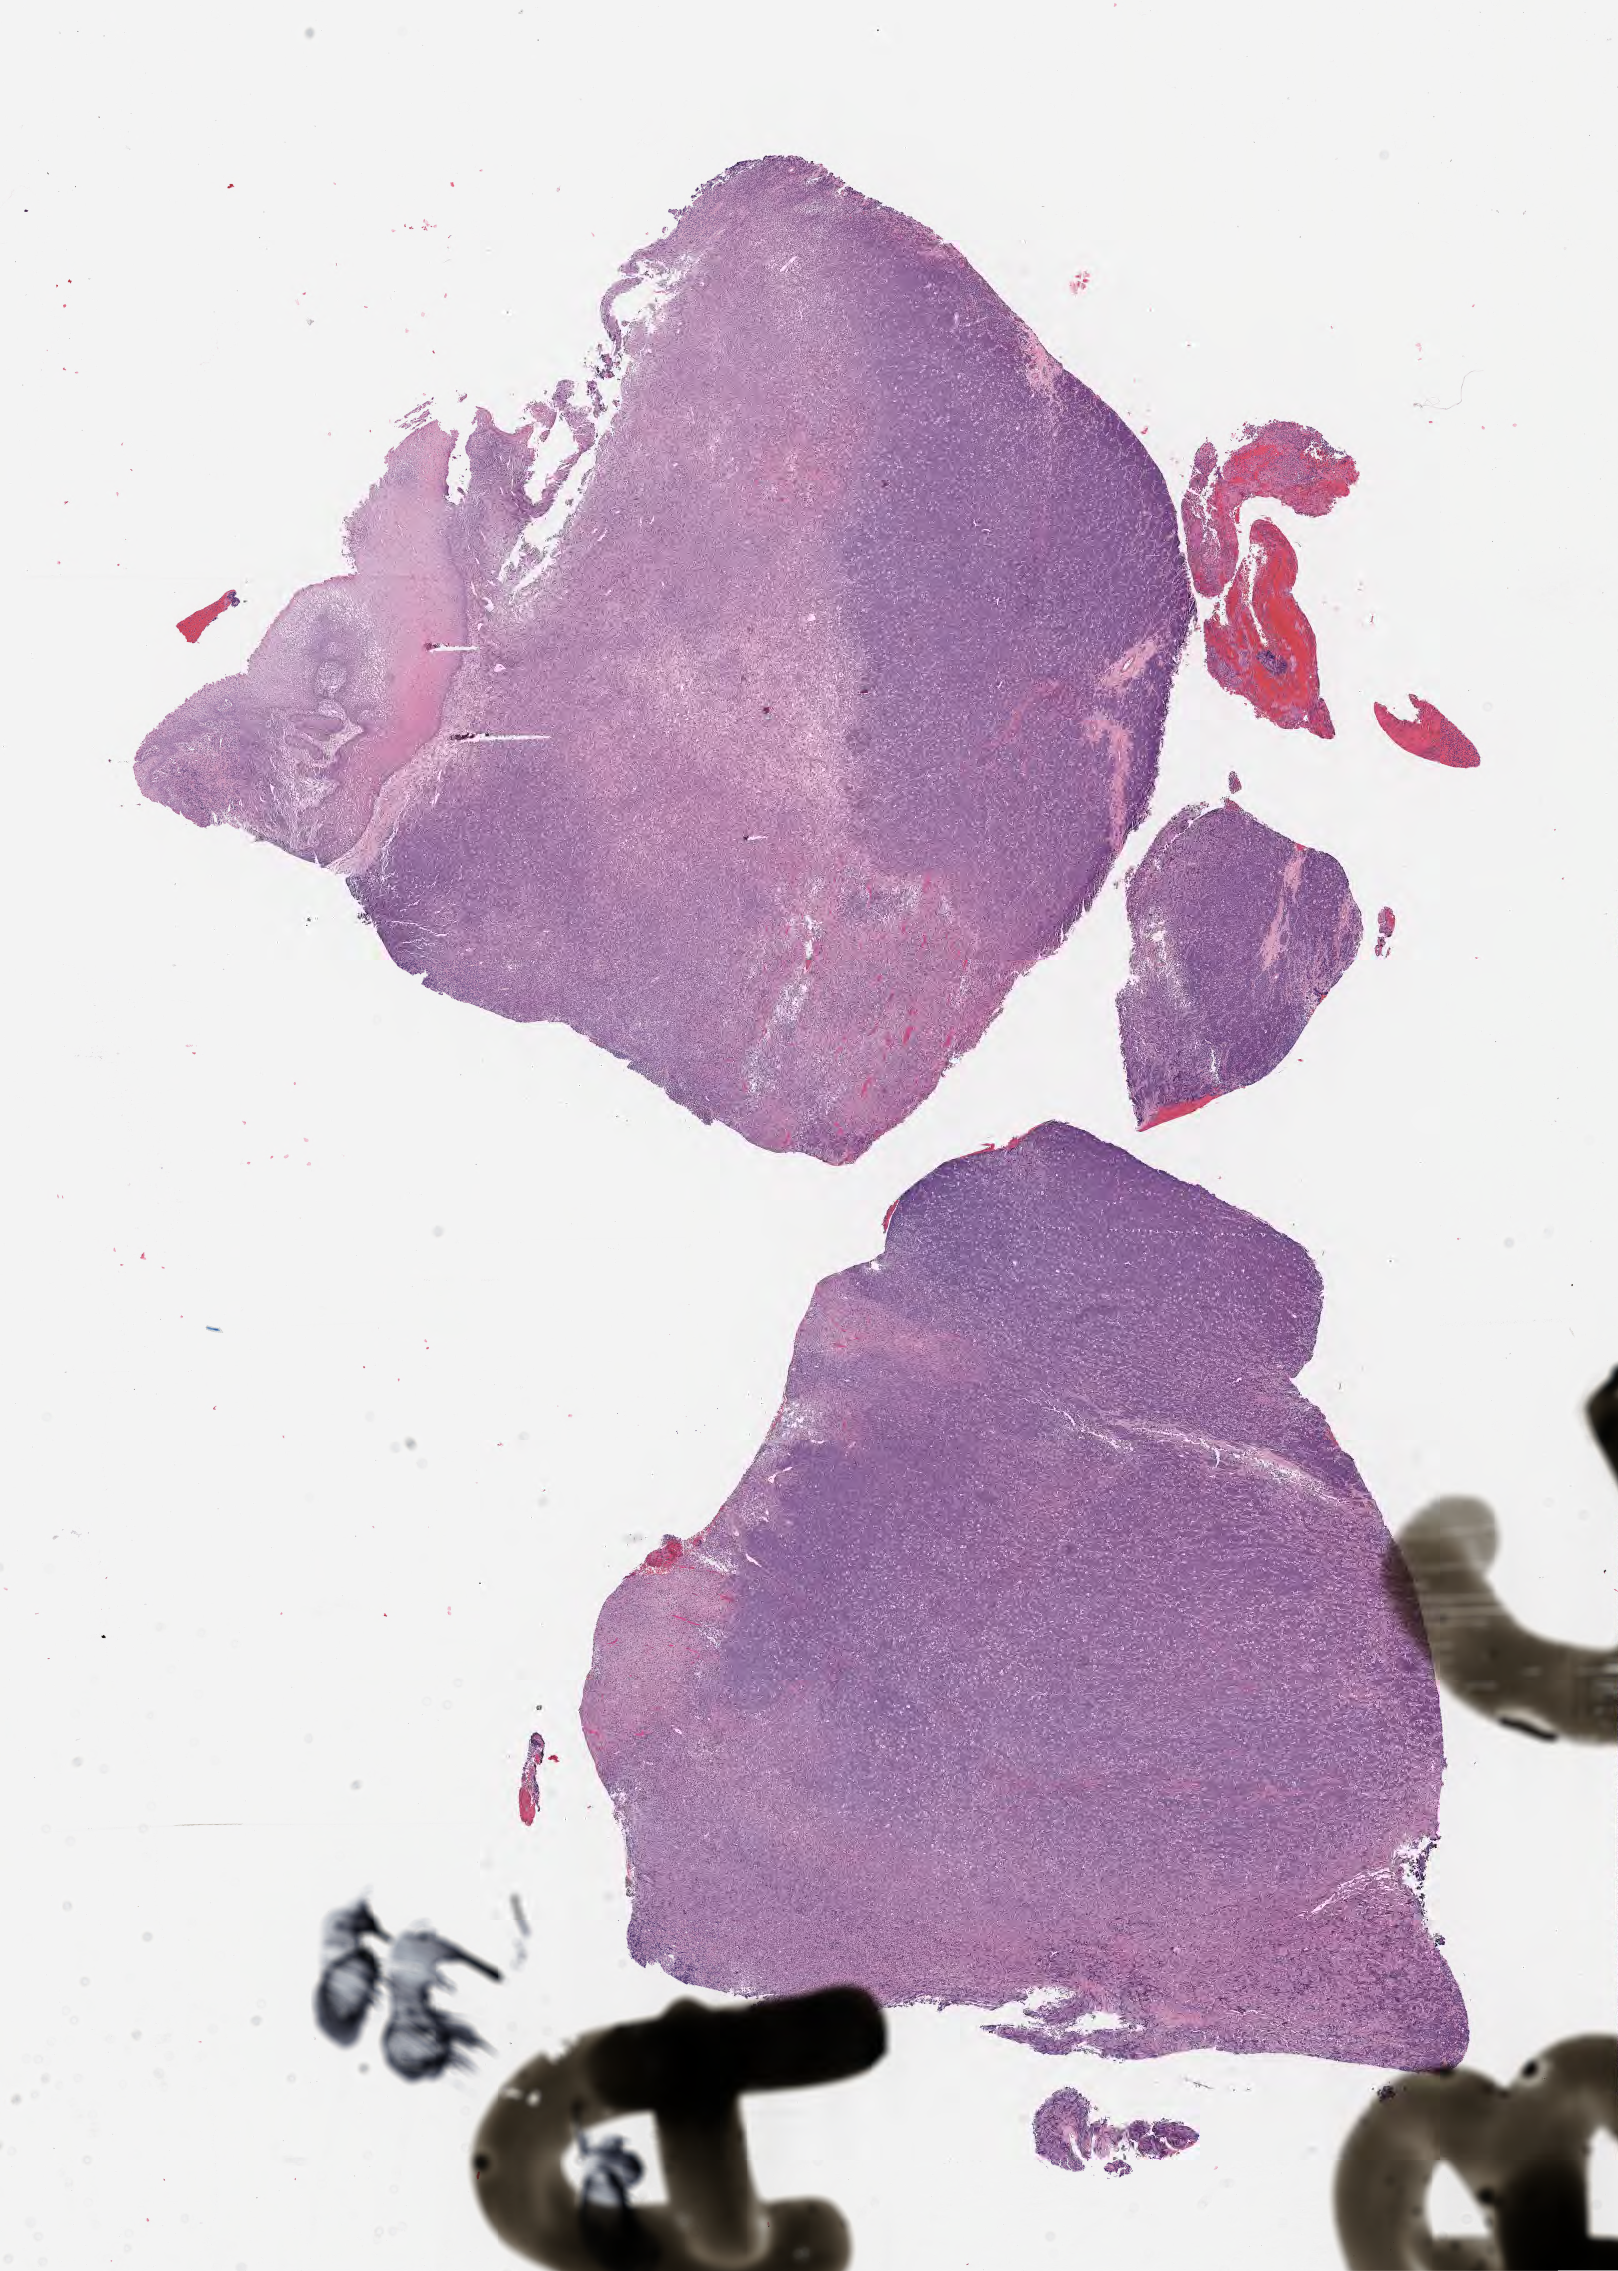
Digitized H&E-stained section — shown as a low-resolution overview of the whole scanned area (about 13.1 x 18.4 mm), formalin-fixed, paraffin-embedded (FFPE) tissue, primary tumor, anatomic site: mandible. Male, age 6 years at initial diagnosis. Composition of this section per pathologist review: tumor cells 60%, tumor nuclei 80%, stromal cells 10%, necrosis 20%, normal cells 10%. Inflammatory infiltration, as recorded: lymphocyte infiltration 30%, monocyte infiltration 40%, neutrophil infiltration 5%.
Ann Arbor stage (patient): Stage IV. Diagnosis: Diffuse large B-cell lymphoma, NOS.